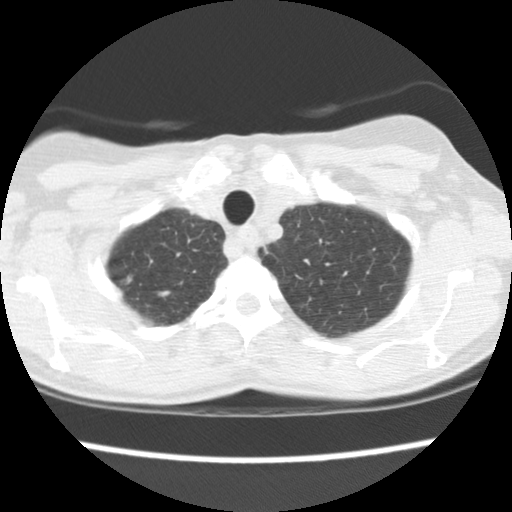
Low-dose screening chest CT, one axial slice; position 131 of 148 along the scan axis; lung window (W 1500 / L -600 HU); 512 × 512 image matrix, field of view 289 × 289 mm.
Annotated regions visible in this slice (outlined manually by an expert reader):
- lesion 1 (tumor): bounding box <126,276,132,284> (left, top, right, bottom; pixels)